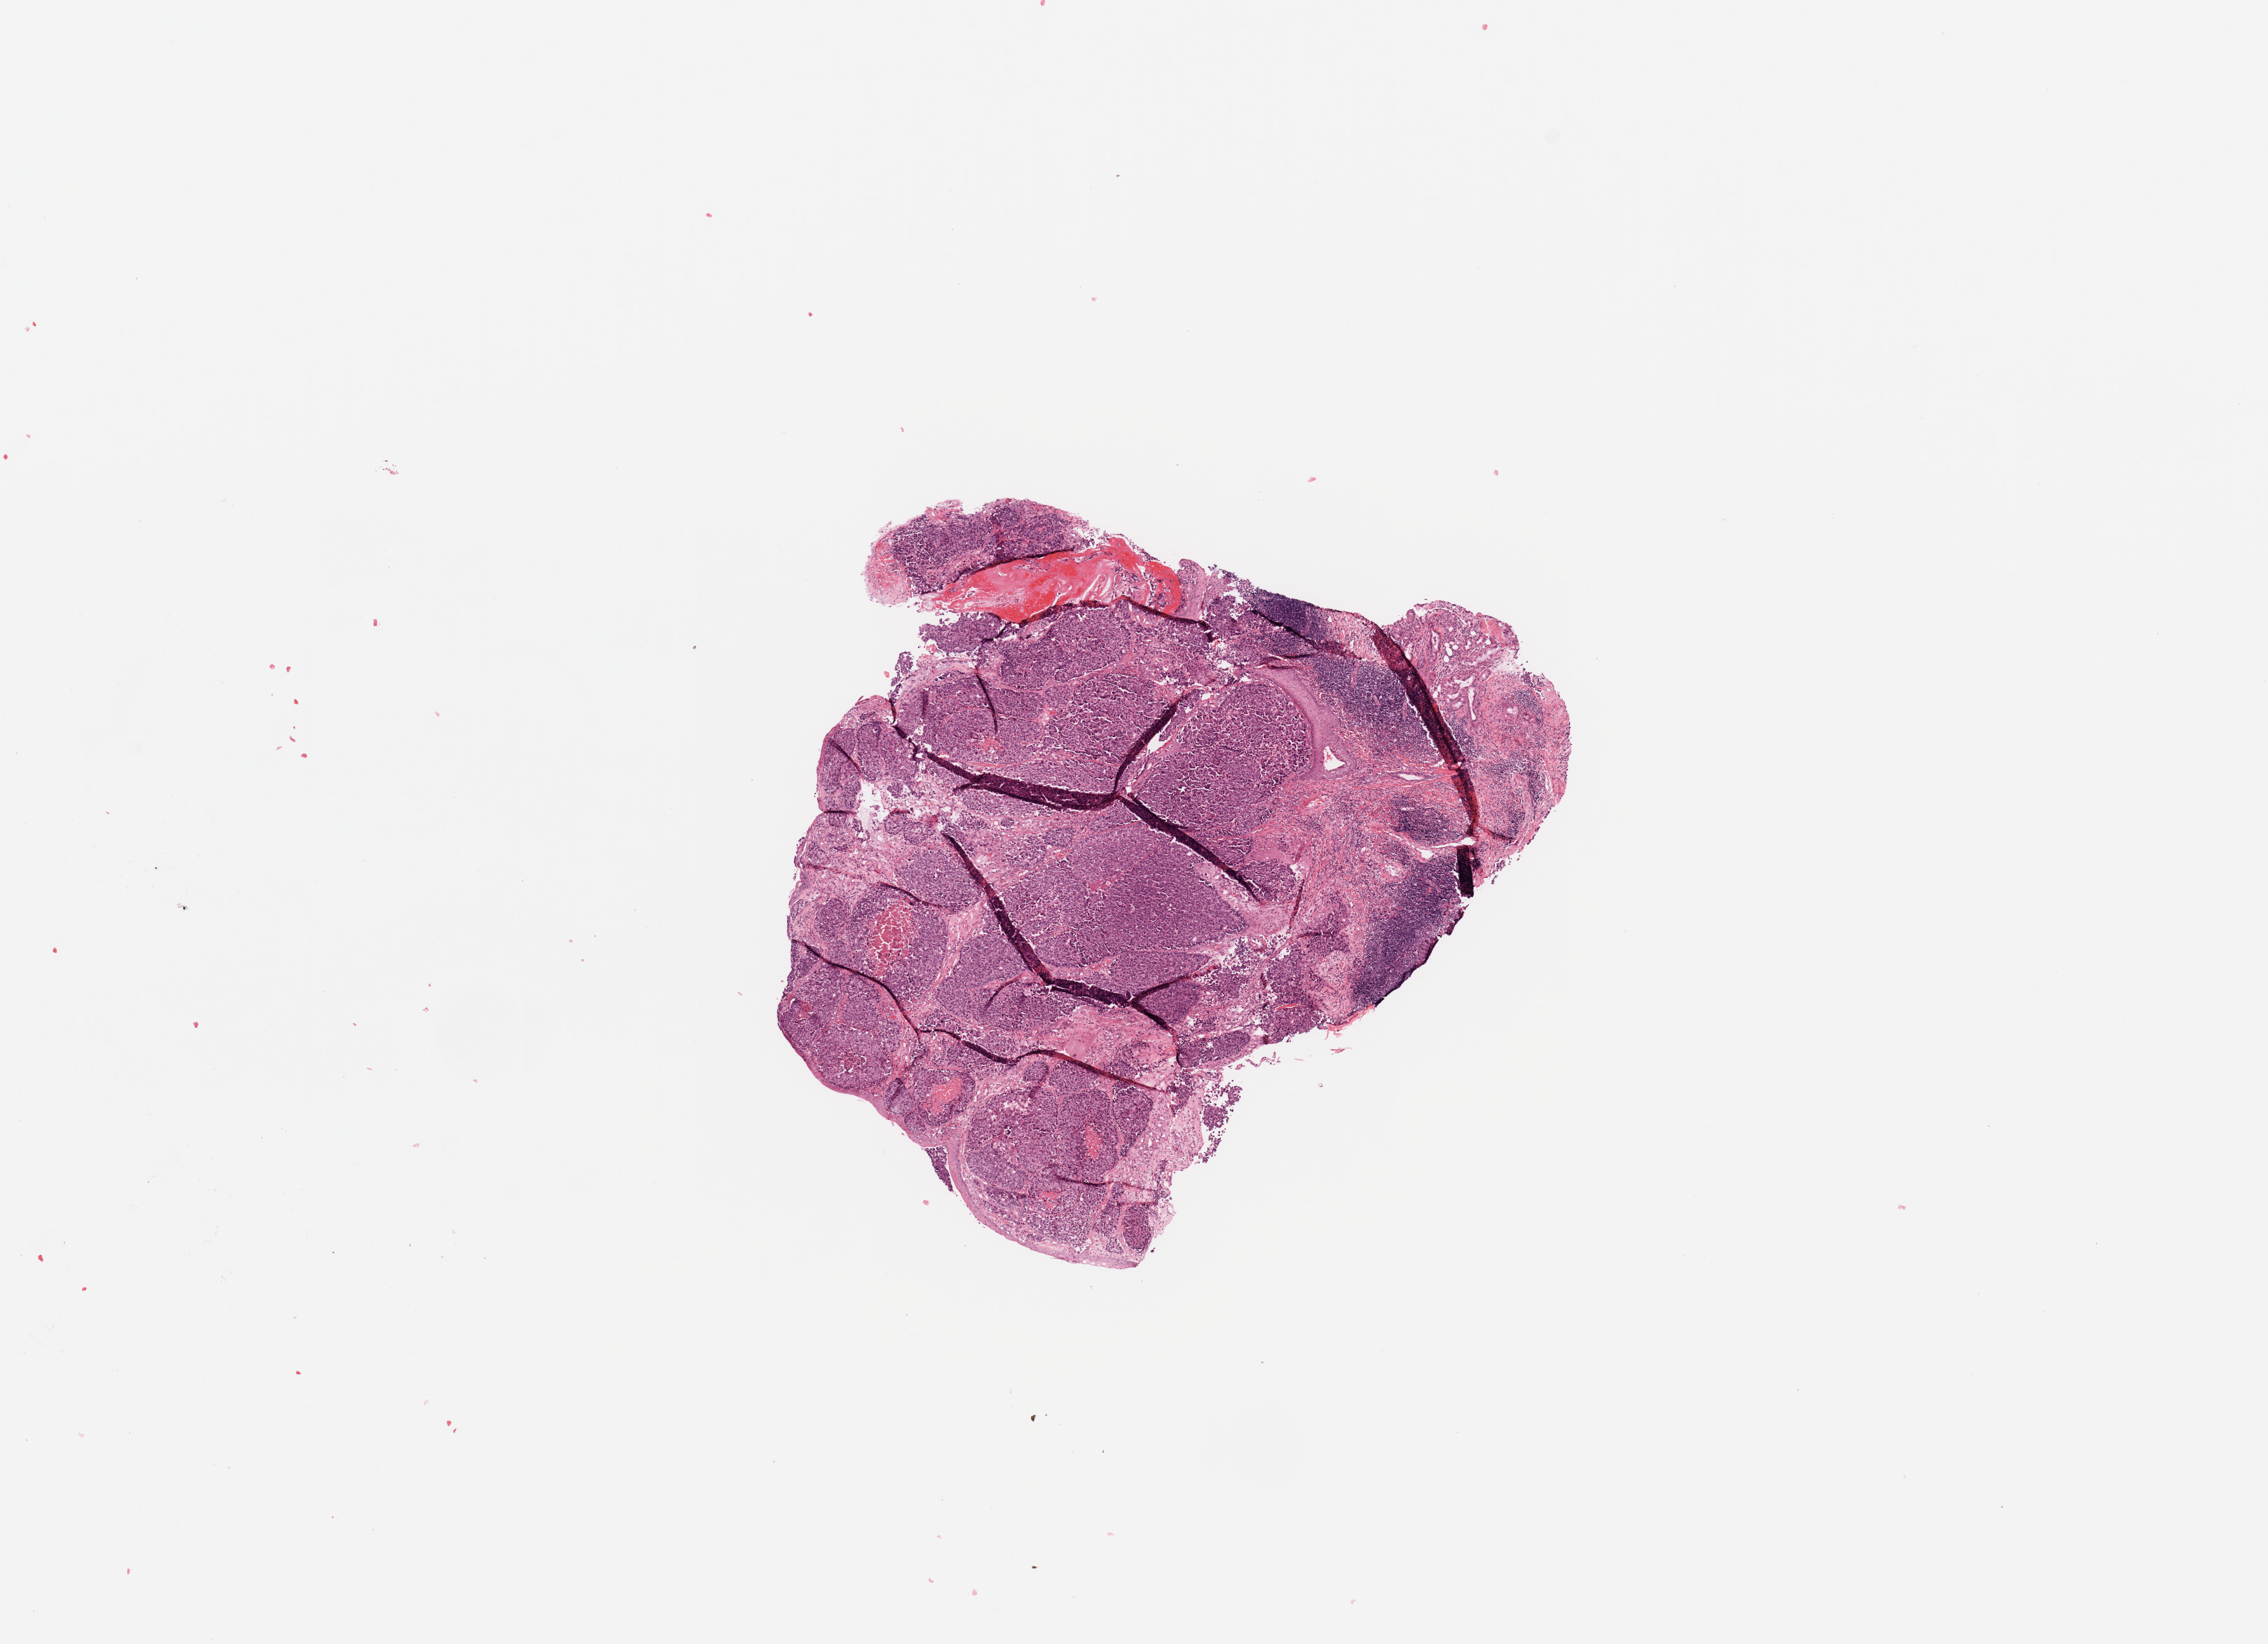
Digitized H&E-stained tissue section (whole slide), a low-resolution overview of the entire scanned area, about 12.8 x 9.3 mm (acquisition: 20x scan). Tumour tissue sample, sampled site: larynx. Female, 63 y/o.
Diagnosis: Squamous cell carcinoma, NOS.